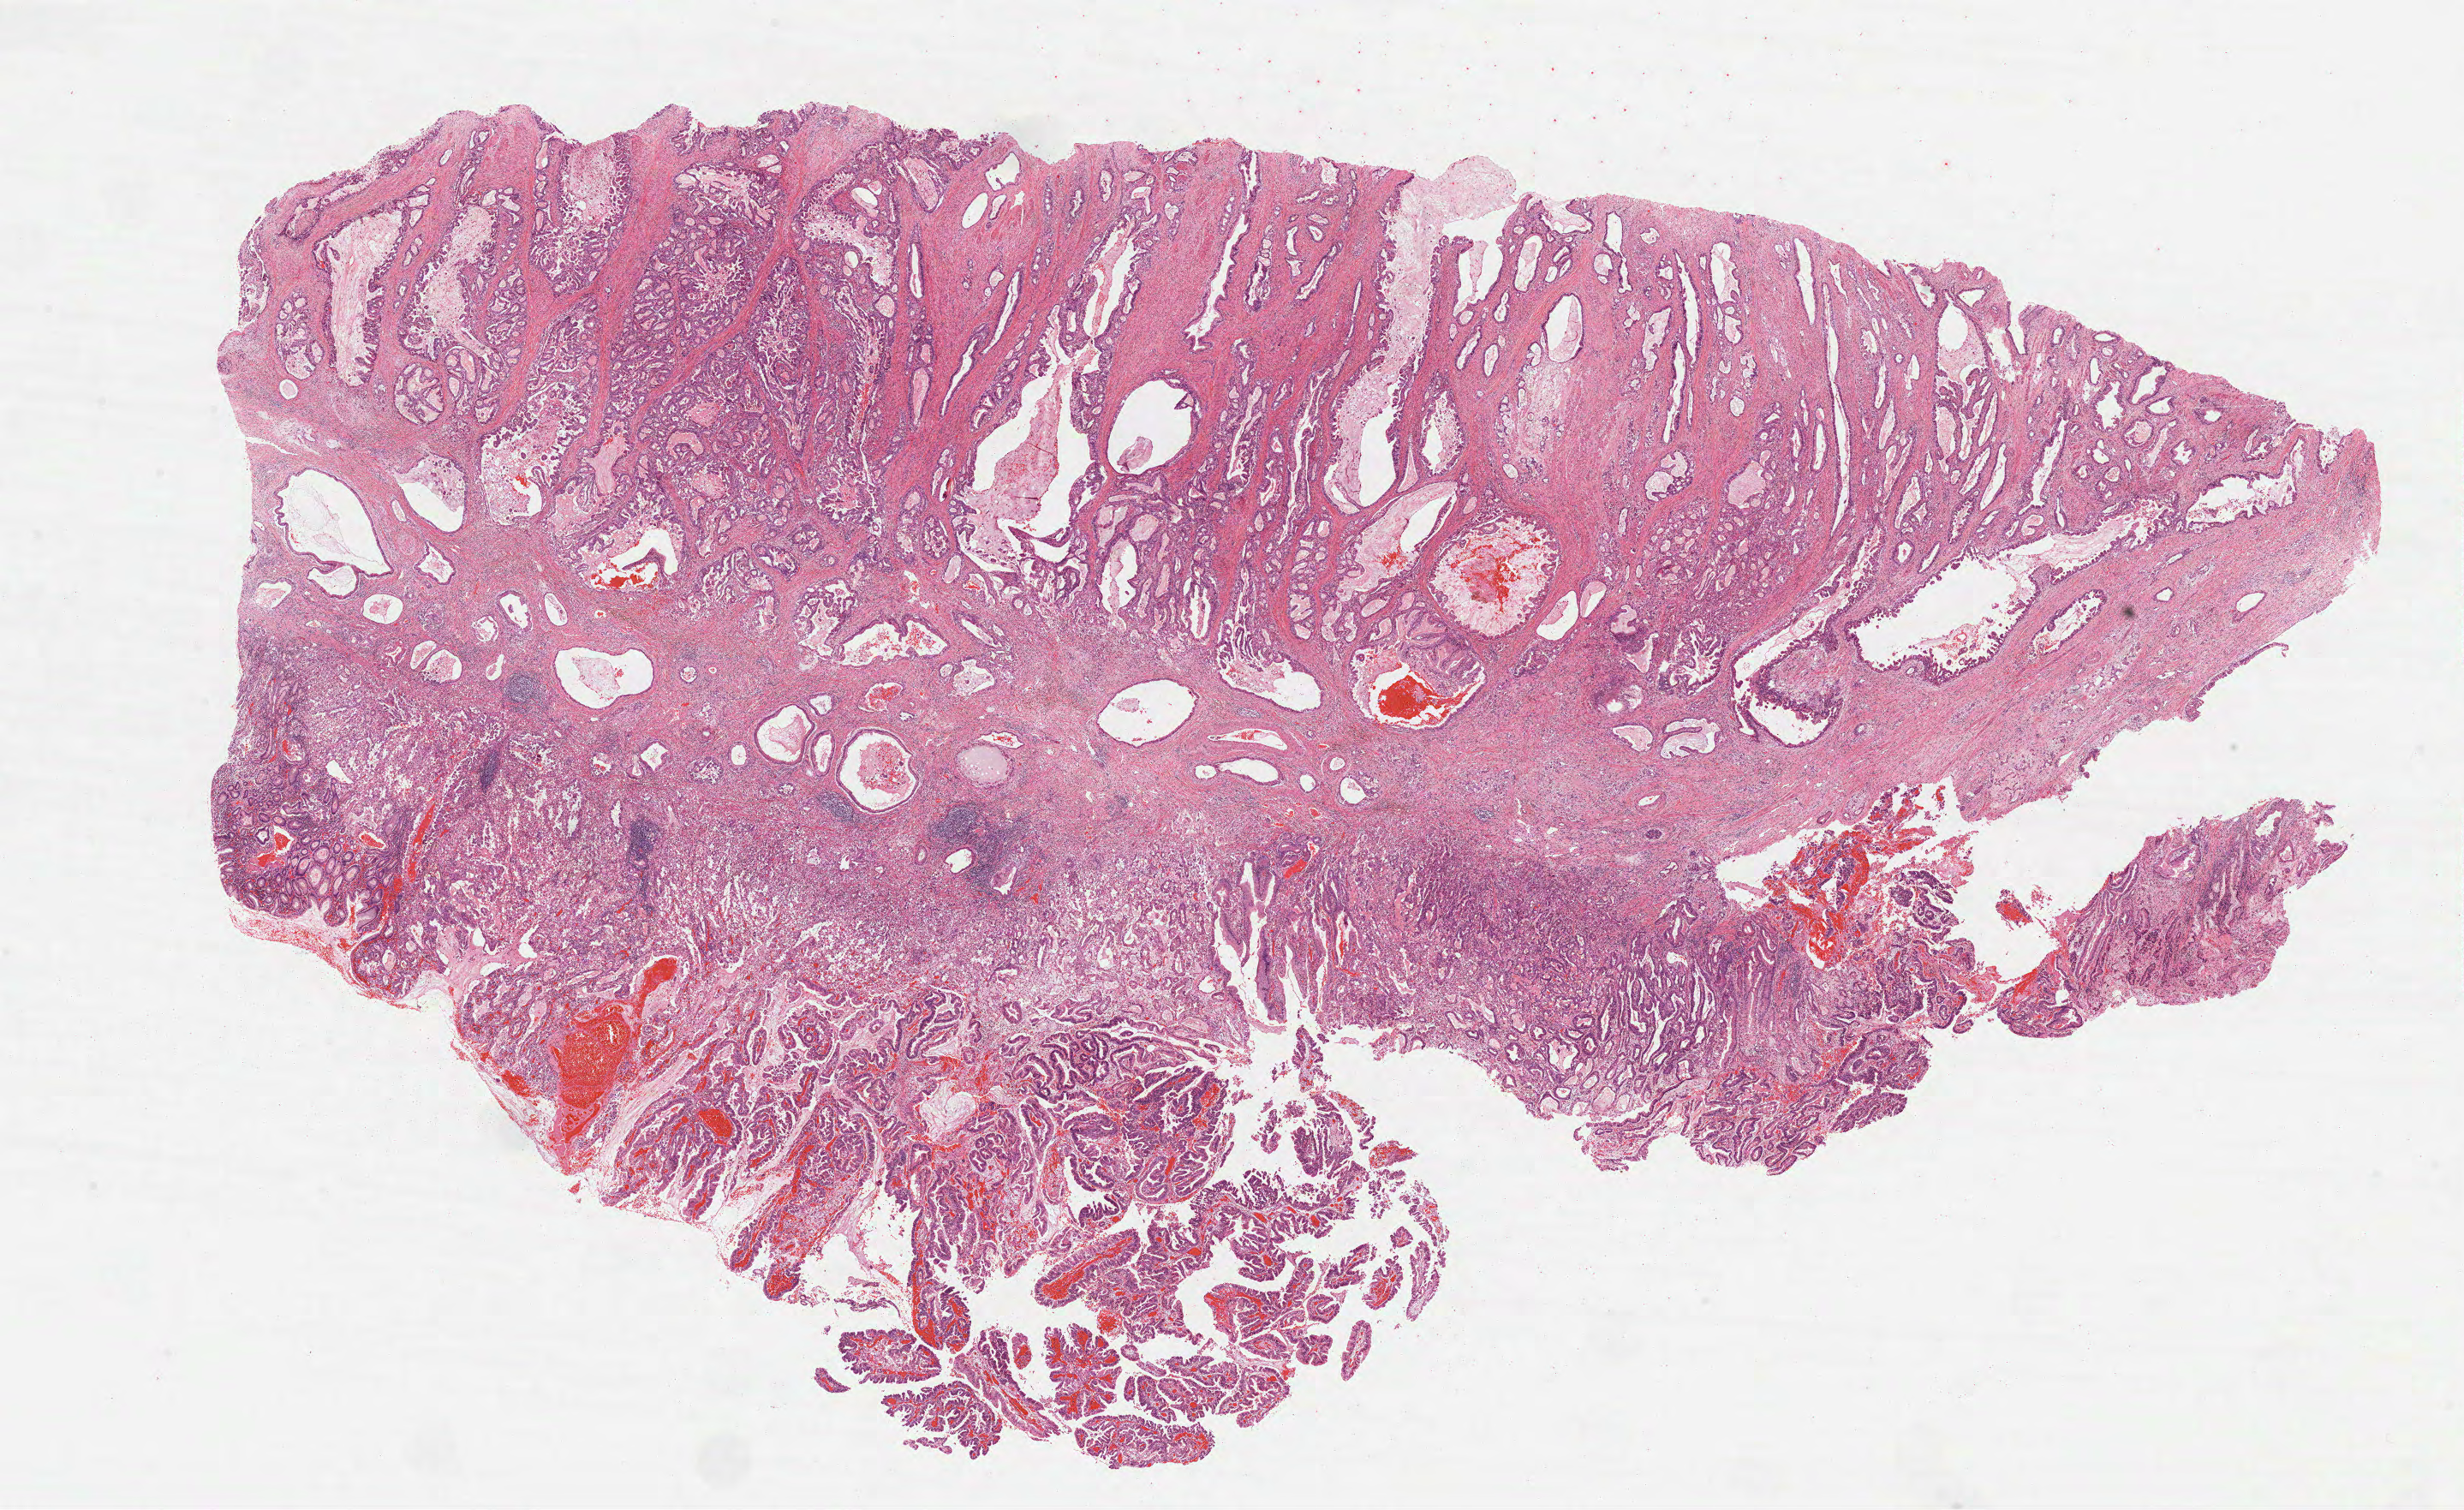
Whole-slide histology image, Hematoxylin and eosin (H&E) stained, whole scanned area (about 23.2 x 14.2 mm, from a 40x scan) shown as a low-resolution overview, FFPE section, sample: primary tumour, stomach. Patient: female, age at initial diagnosis 67 years. Histologic grade: G3 (poorly differentiated).
• lymph nodes positive (case pathology): 5 of 9 examined
• AJCC pathologic stage: IIIC (7th edition)
• histologic diagnosis: Adenocarcinoma, NOS (cardia, NOS)